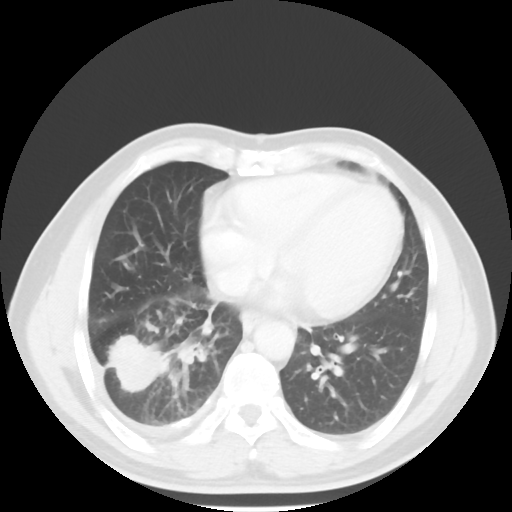
Chest CT, one axial slice. Position 21 of 56 along the scan axis. 120 kVp. Lung window (W 1500 / L -600 HU). 5 mm slice thickness. 512 × 512 image matrix. Male patient, age 56 years. Case-level facts recorded for this patient, not image findings: clinical TNM (as recorded): T2 N3 M1.
Structures marked on this image (rectangle marked by the reading radiologist):
- lung tumour (recorded histology: adenocarcinoma): bounding box [x1, y1, x2, y2] px = [107, 330, 171, 395]